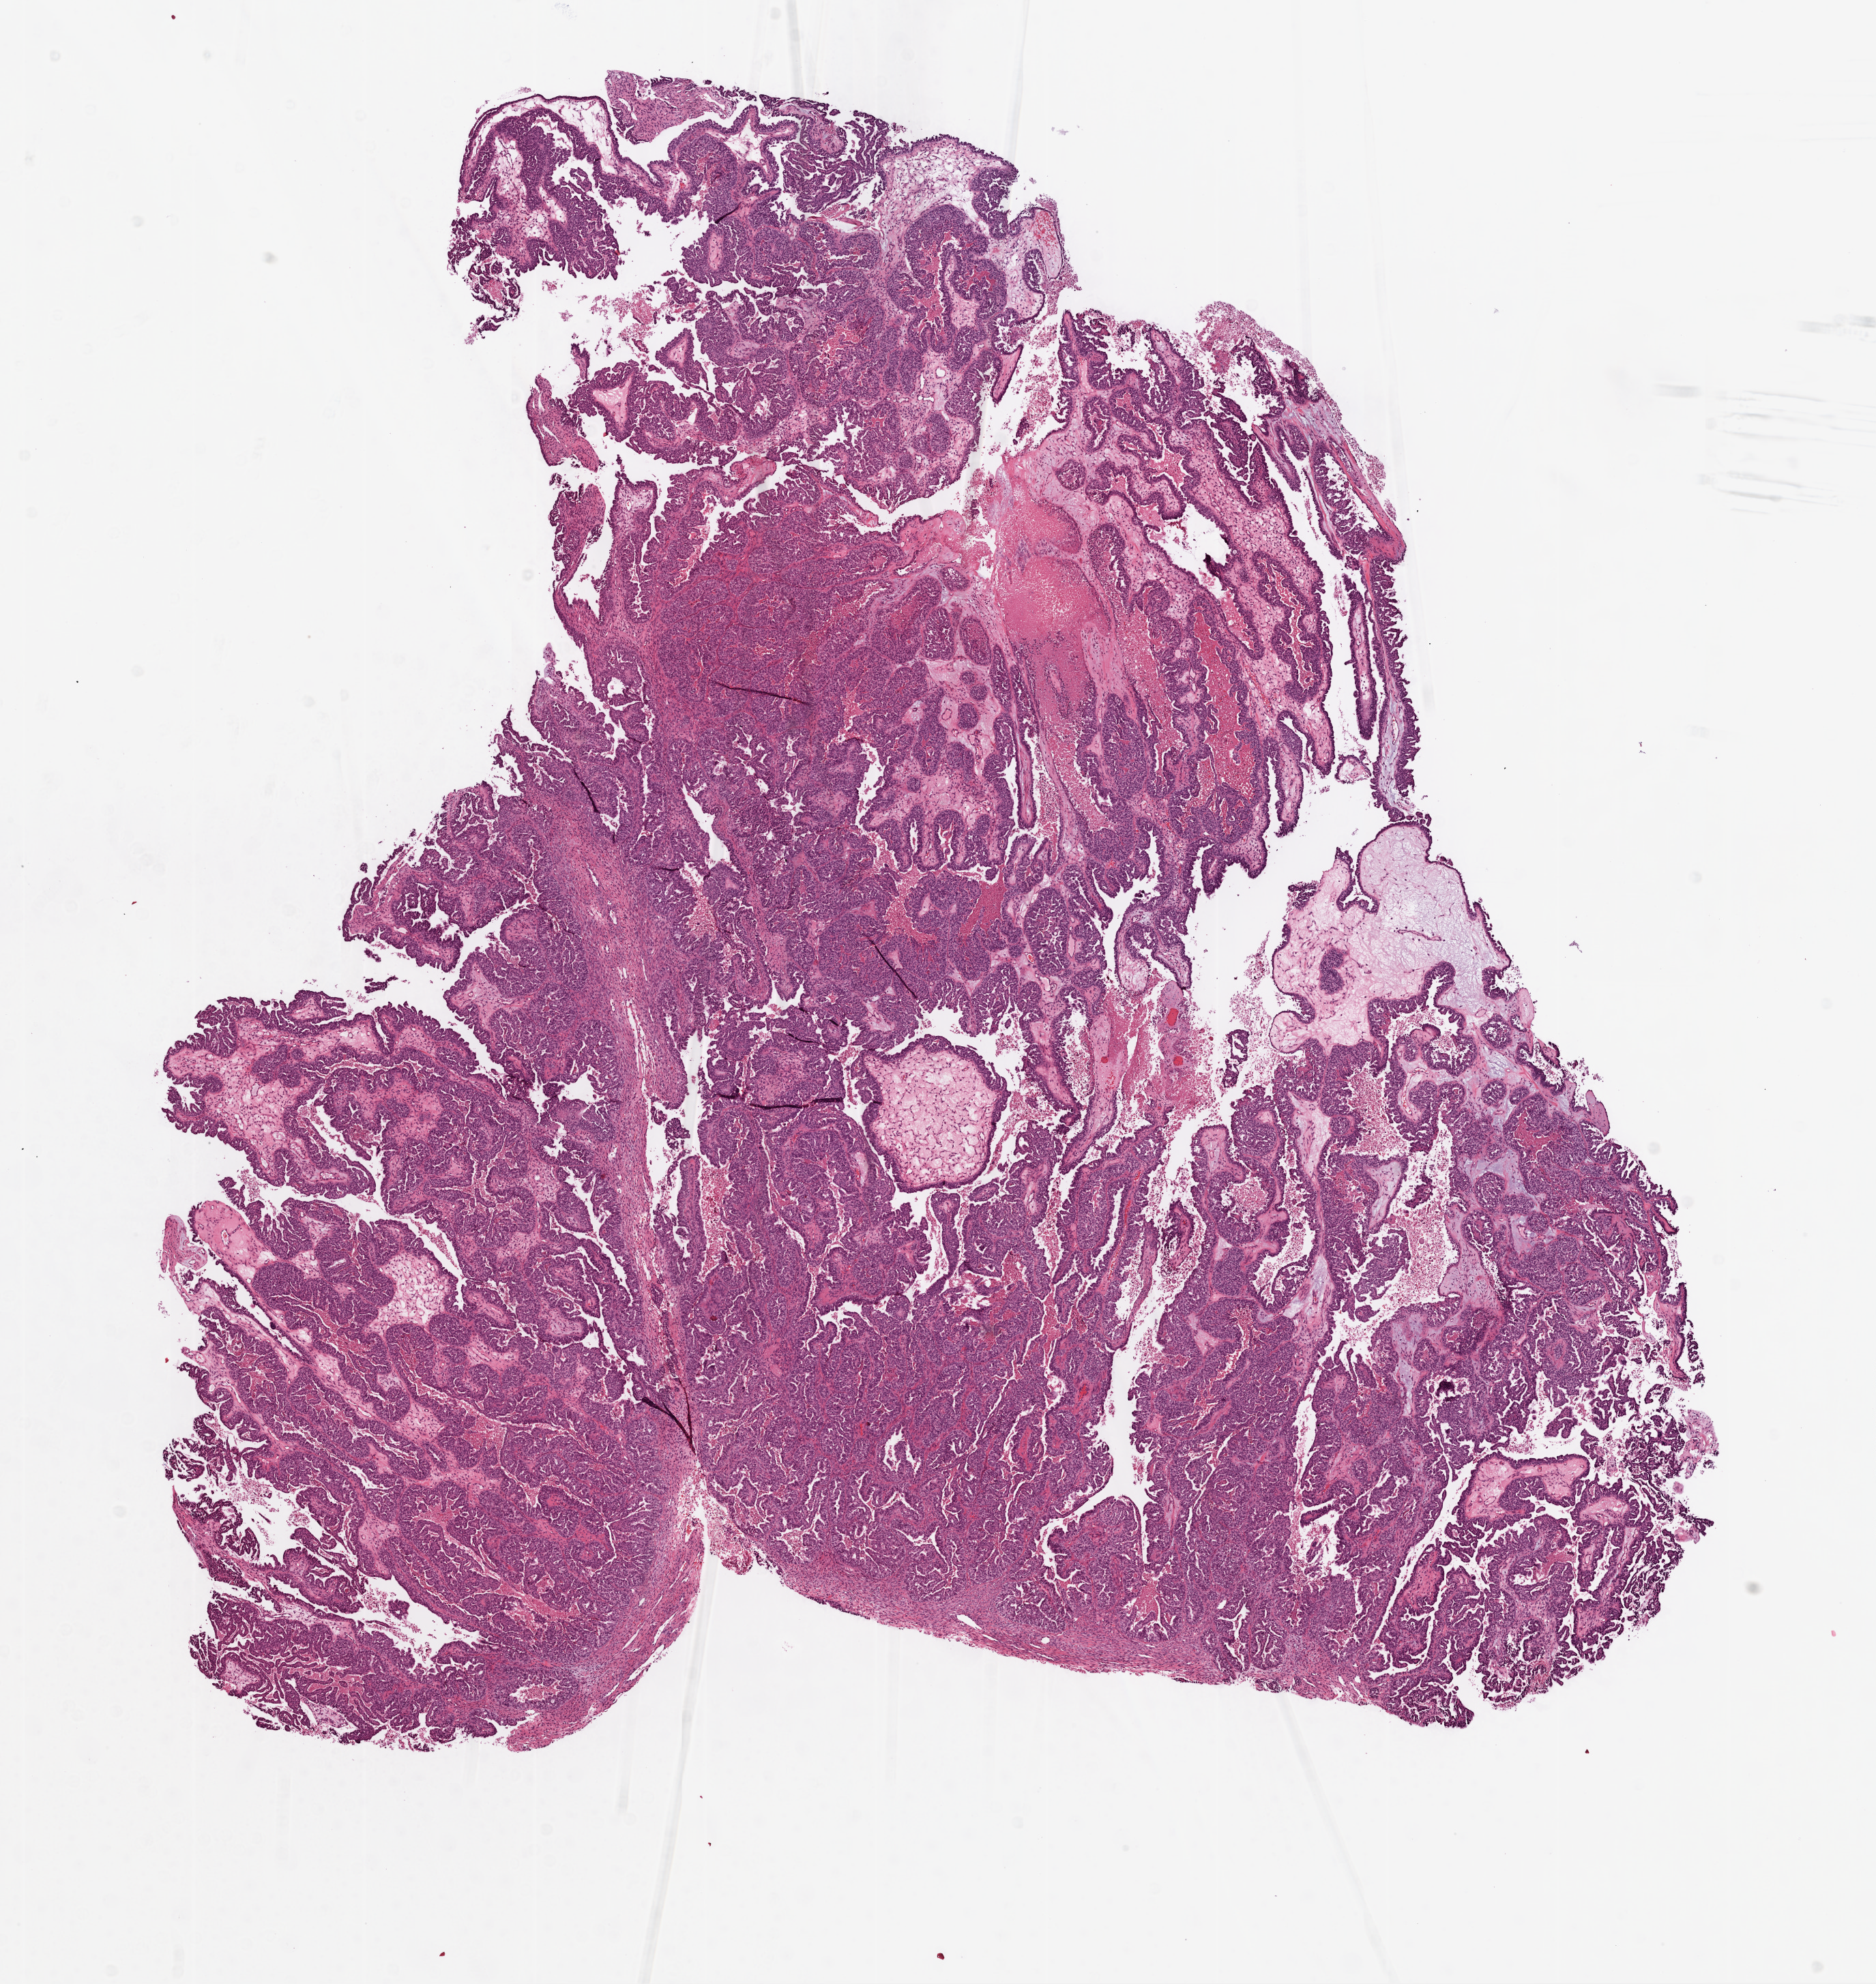
Whole-slide histology image, H&E, a low-resolution overview of the entire scanned area, about 11.0 x 11.7 mm. Frozen section. Primary tumour sample from the ovary. Patient: female, age at initial diagnosis 51 years. Histologic grade: GX (grade cannot be assessed). Composition of this section per pathologist review: tumour cells 80%, tumour nuclei 95%, normal cells 0%, stromal cells 15%, necrosis 5%.
Laterality: bilateral. Diagnosis: Serous cystadenocarcinoma, NOS. FIGO stage: IIIC.